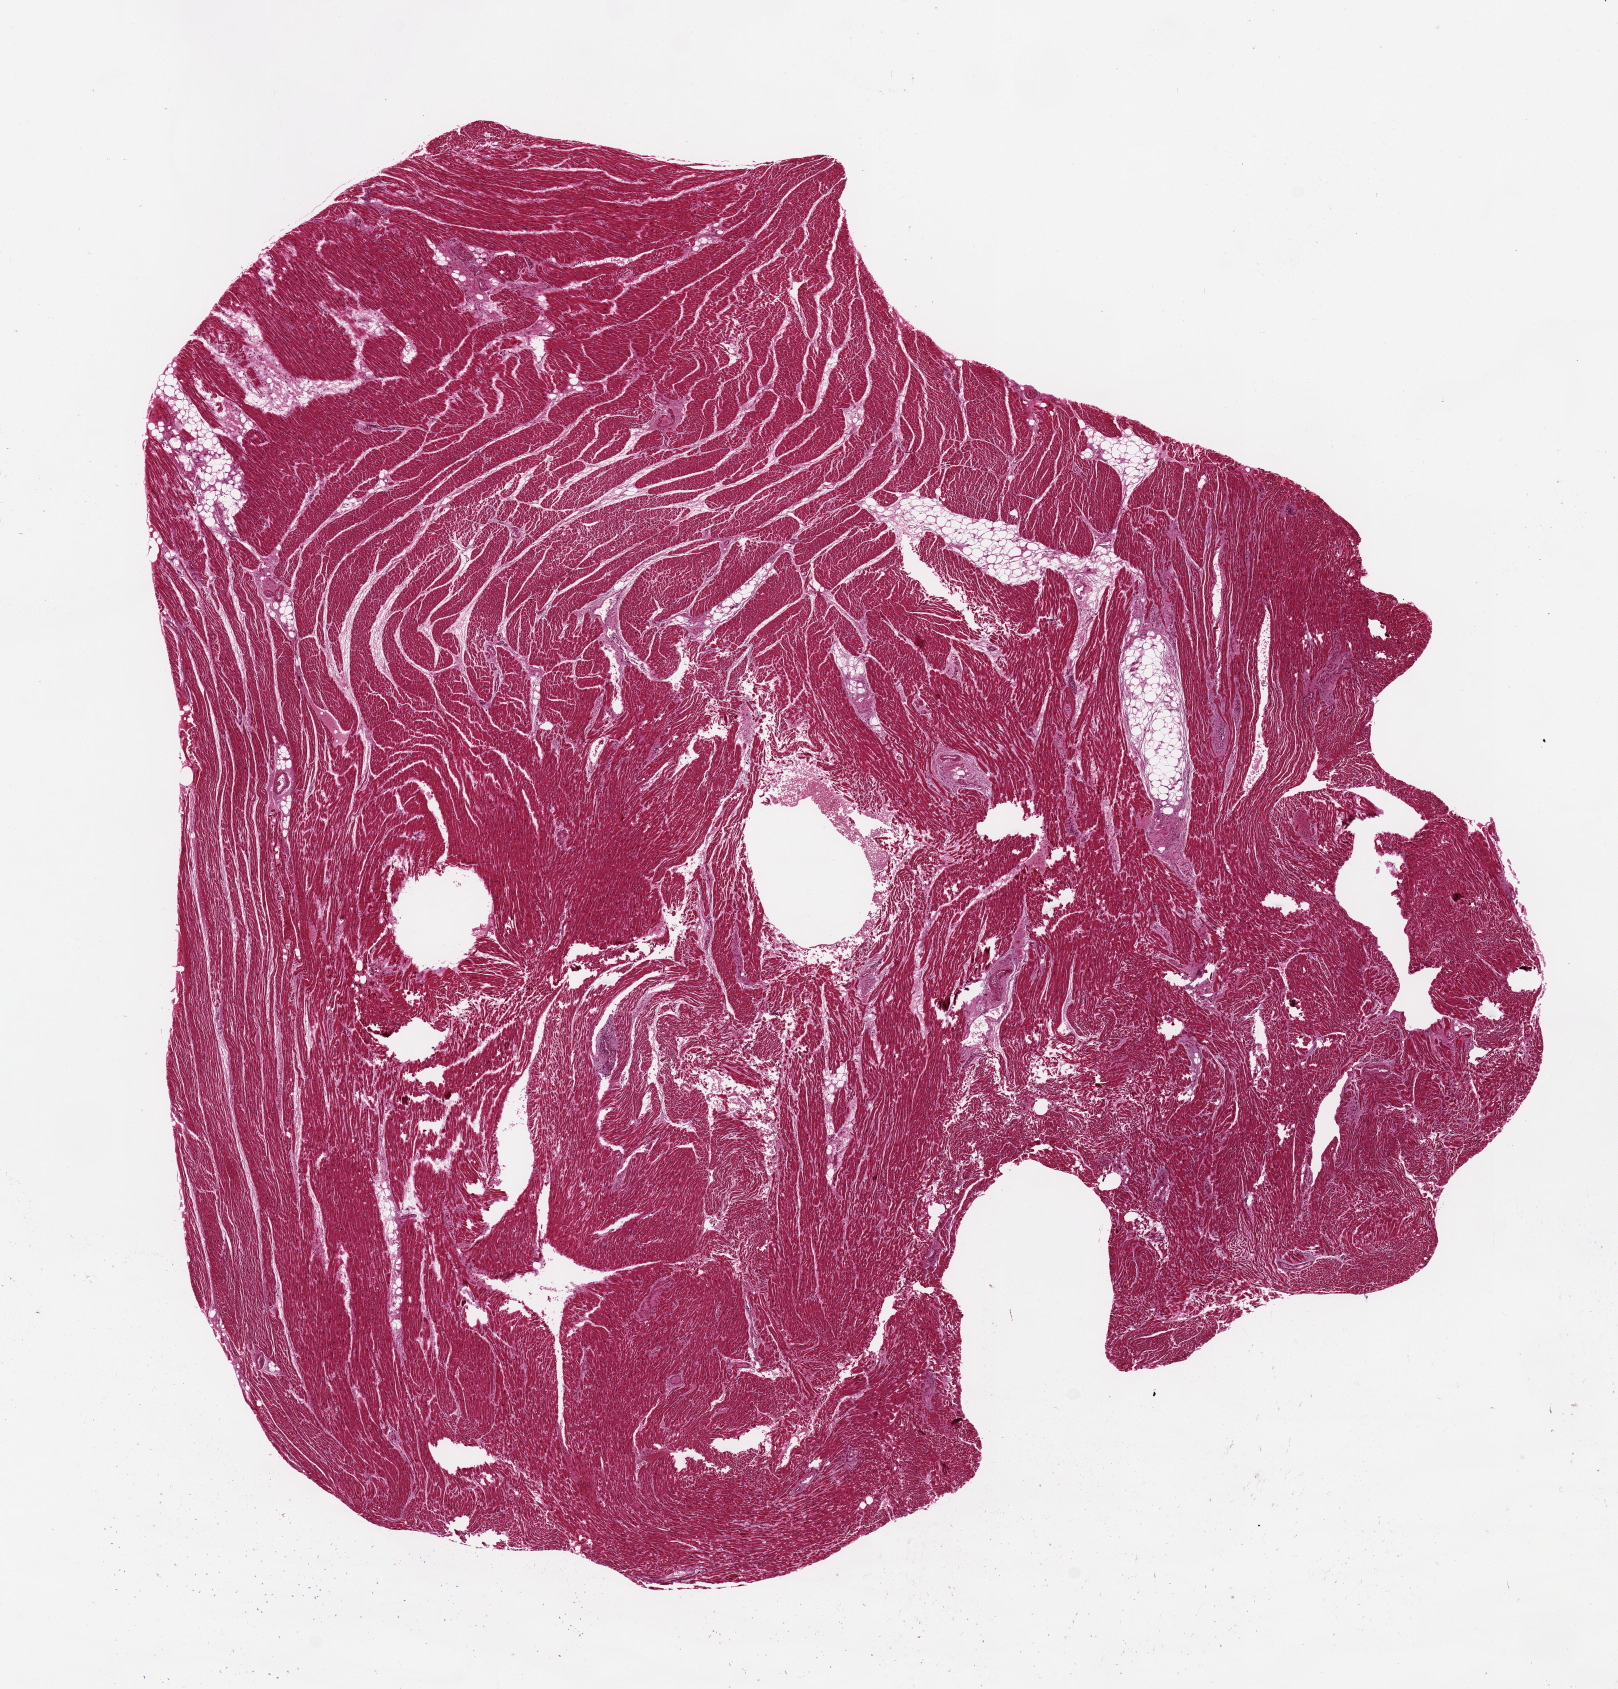
Hematoxylin and eosin (H&E) whole-slide image — shown as a low-resolution overview of the whole scanned area (about 12.8 x 13.4 mm). PAXgene-fixed, paraffin-embedded tissue. Target tissue: heart. Tissue donor sample. Donor sex: female.
Reviewer comment on this tissue sample: 11x11mm. Moderate fractures.